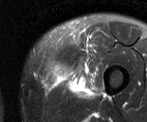
MRI of an extremity soft-tissue mass, one axial slice; position 10 of 52 along the scan axis; T2-weighted fat-saturated; MR volume resampled by the dataset authors to the PET/CT grid (not the native acquisition matrix); 3.27 mm slice thickness; 147 × 122 image matrix, field of view 144 × 119 mm. Male patient. Case-level facts recorded for this patient, not image findings: histological type: pleiomorphic liposarcoma; grade: high; site of the primary tumour: left thigh.
Structures marked on this image (expert contour drawn on MRI and transferred to this co-registered scan by the dataset authors):
- gross tumour volume including surrounding oedema: bounding box [x1, y1, x2, y2] px = [48, 53, 95, 95]
- gross tumour volume (mass): [48, 53, 70, 77]